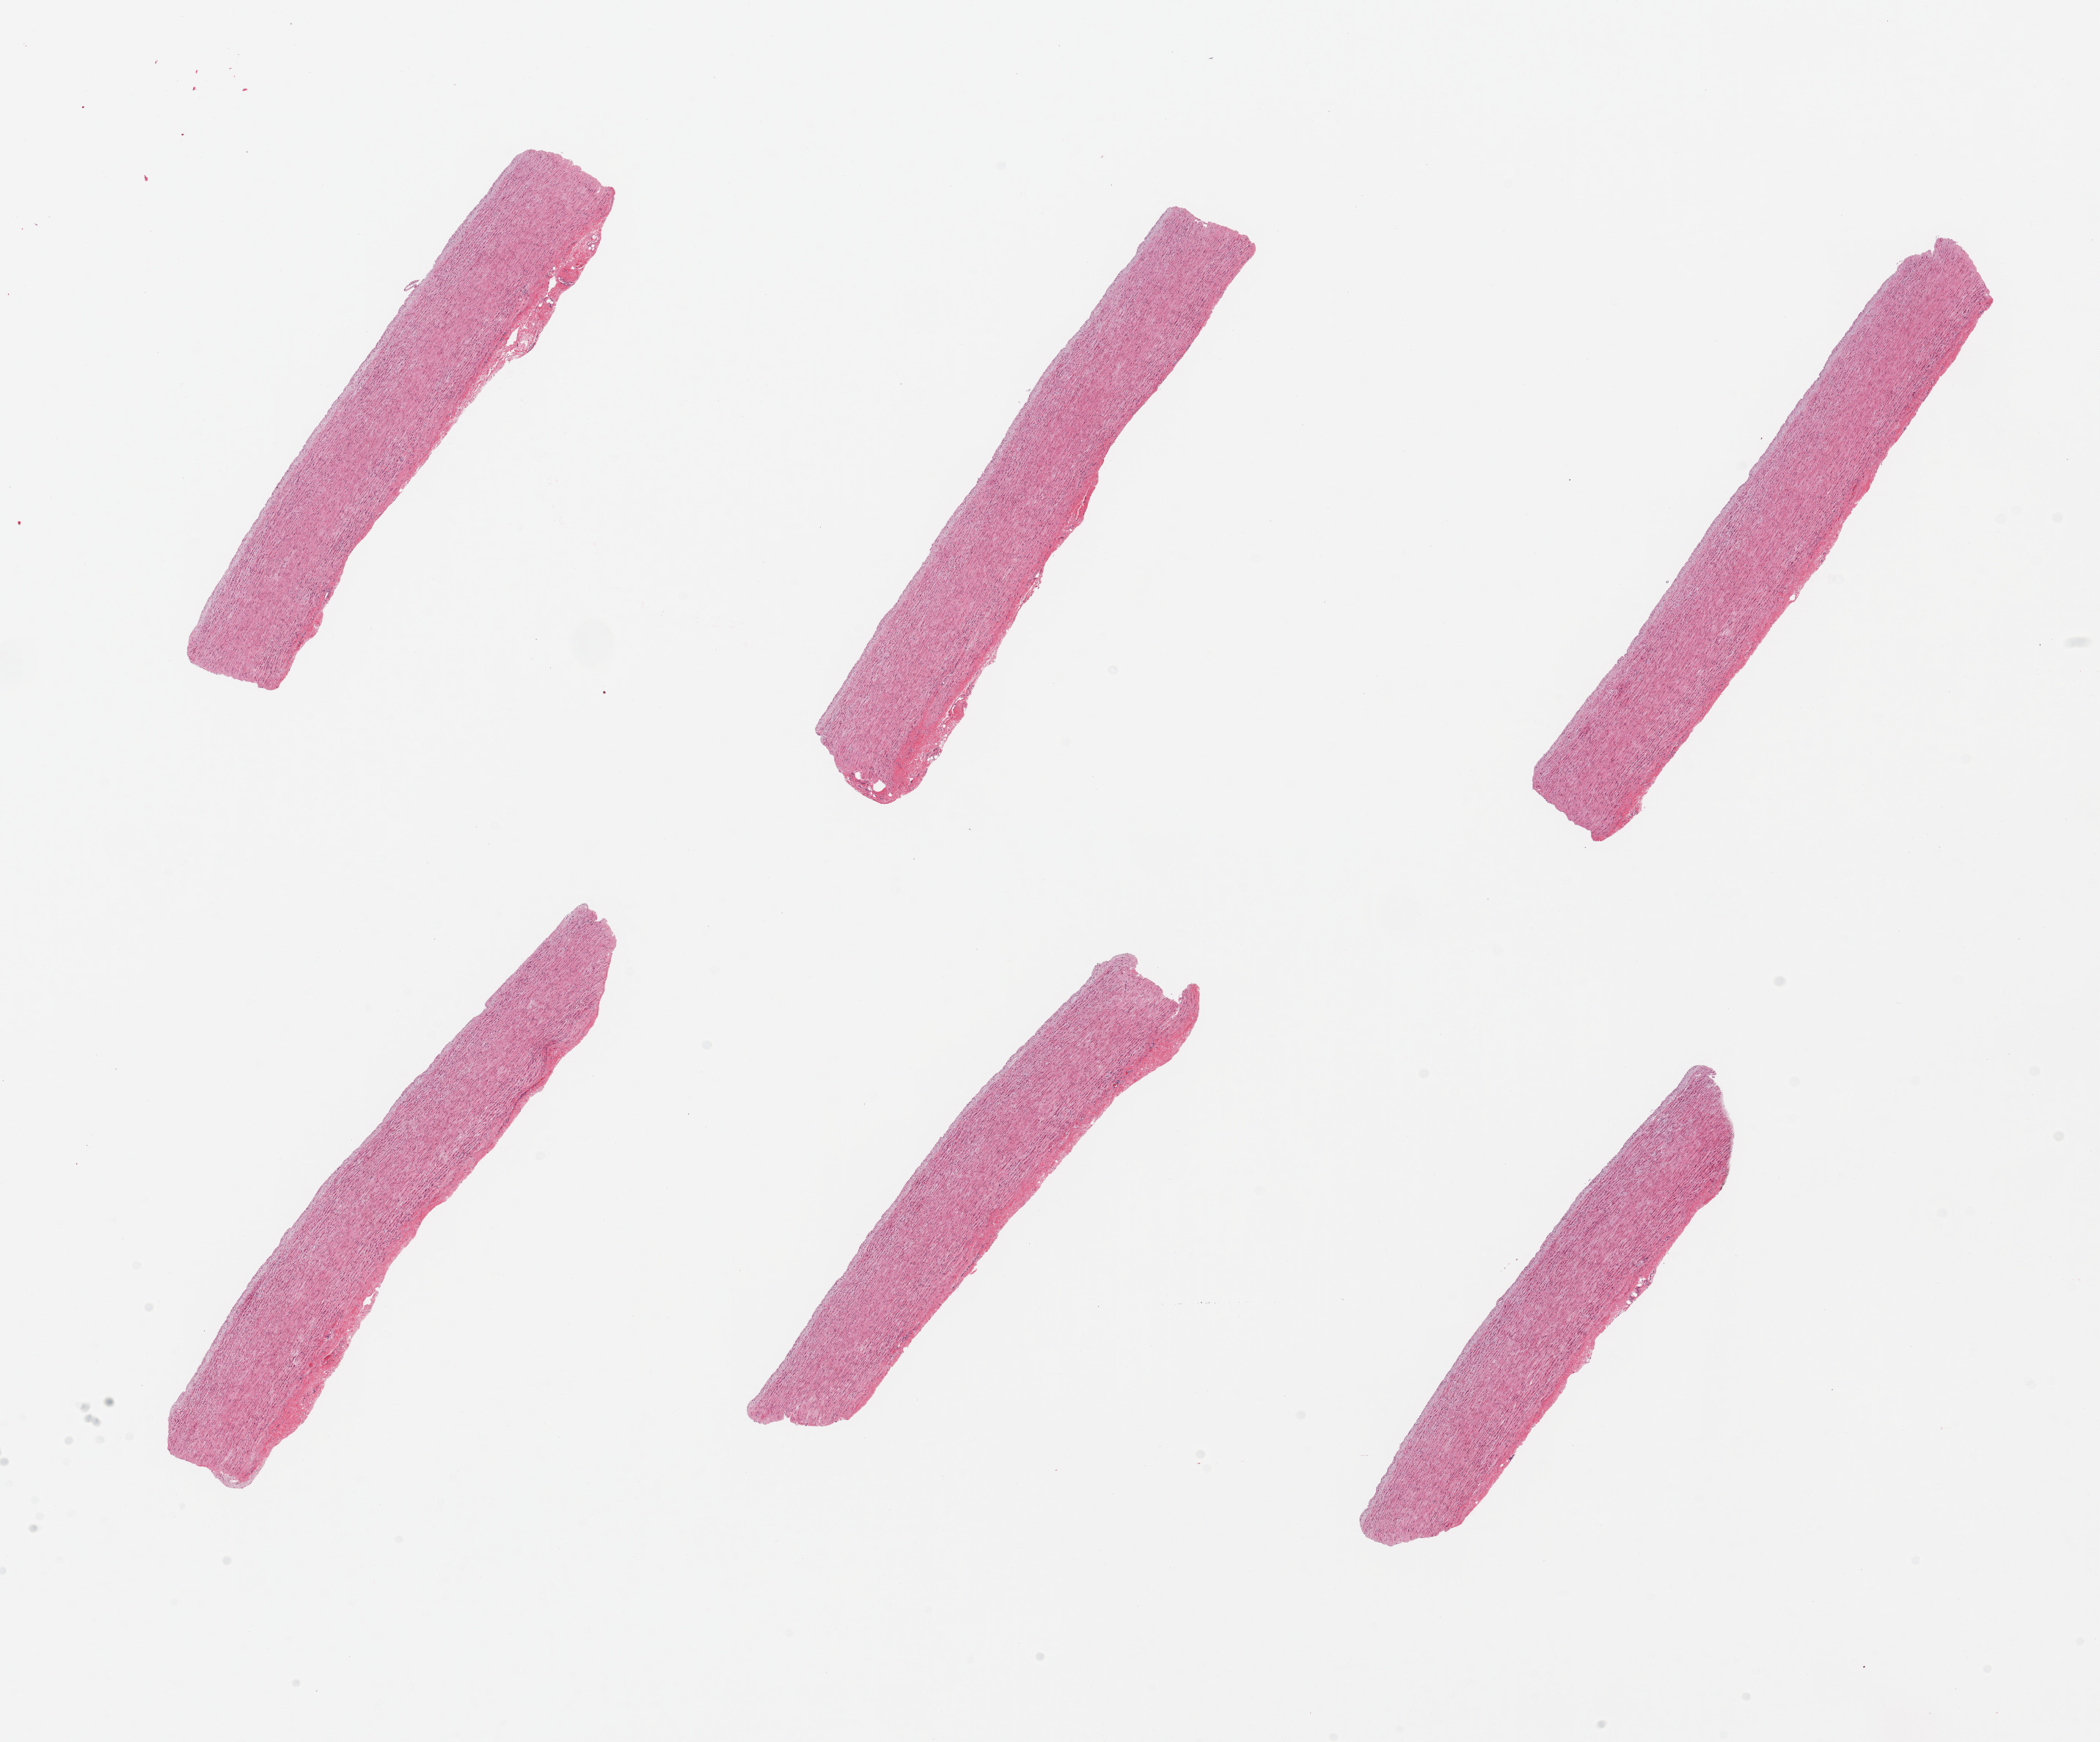
Whole-slide image, H&E stain, brightfield, whole scanned area (about 22.6 x 18.8 mm, acquisition: 20x scan) shown as a low-resolution overview. PAXgene-fixed paraffin-embedded (PFPE) section. Sampled site (target tissue): aorta. Tissue donor sample.
- pathologist's review note for this sample: 6 pieces; well trimmed, no plaques